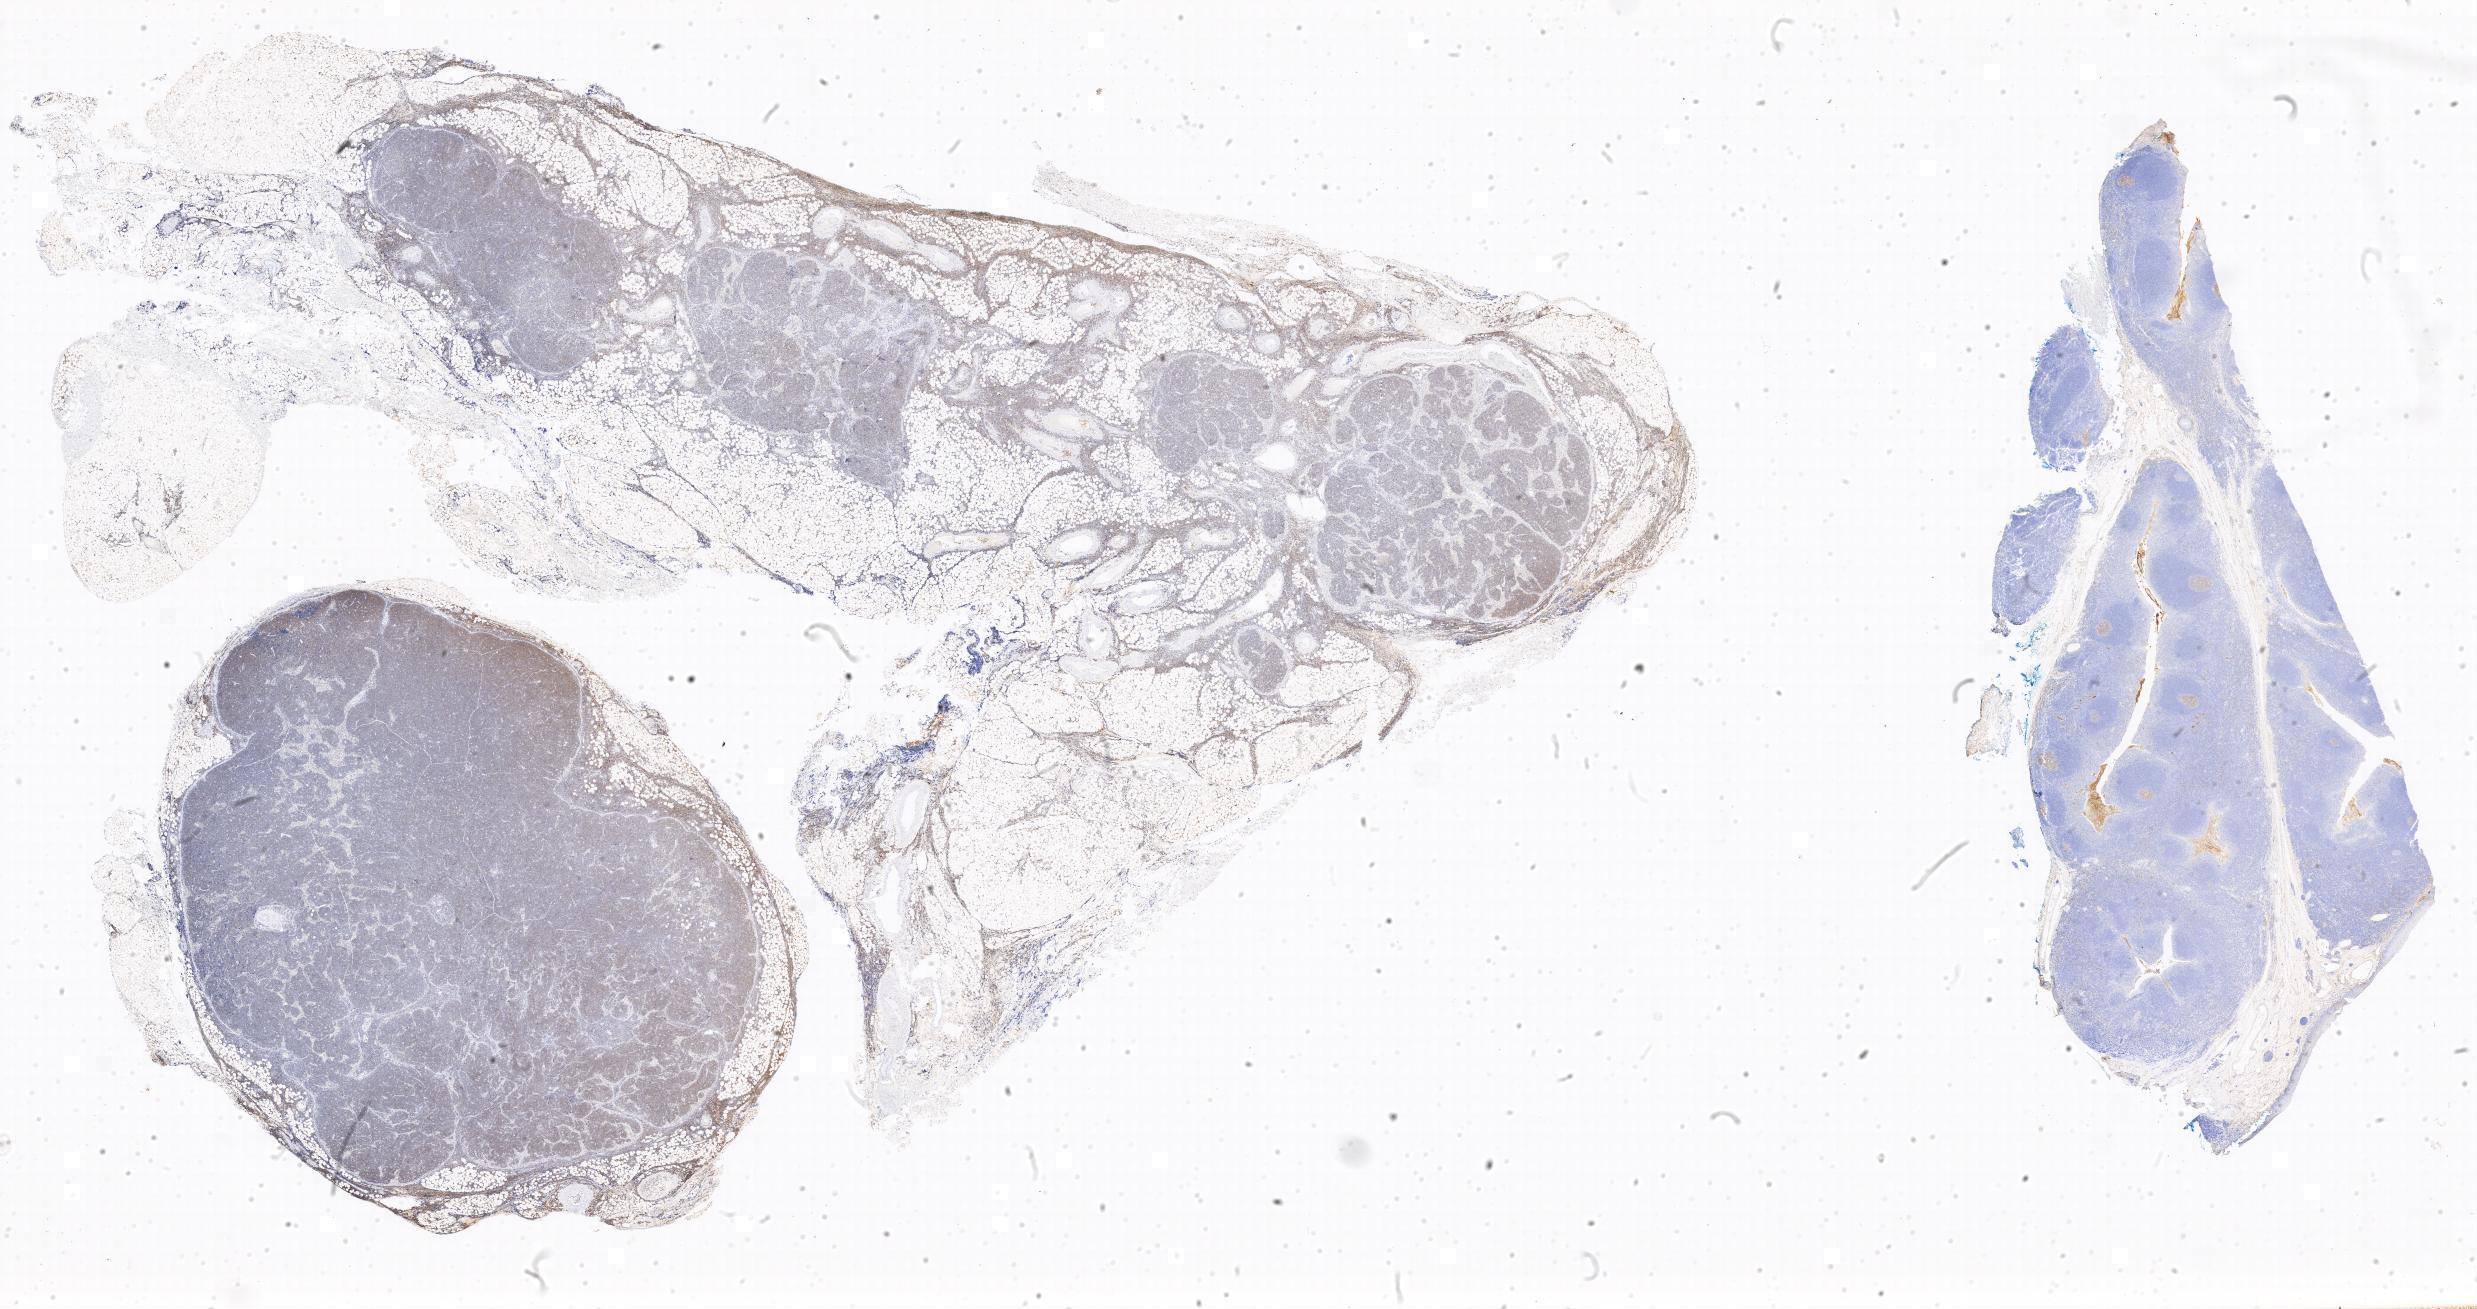
Immunohistochemistry (IHC) whole-slide image stained for CD10, low-resolution overview of the scanned area, specimen: tumor tissue, anatomic site: spleen. Patient: female, aged 15.
Diagnosis: Burkitt lymphoma, NOS.